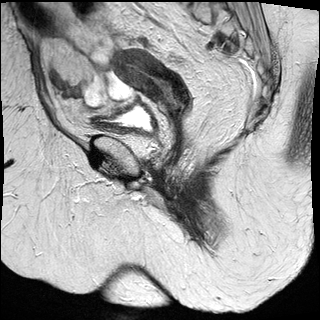
Pelvic MRI for cervical cancer, one sagittal slice. Position 12 of 27 along the scan axis. T2-weighted. 1.5 T. TE 89 ms, TR 2740 ms. 4 mm slice thickness. 320 × 320 image matrix, field of view 260 × 260 mm. Patient: female, 67 years.
Annotated regions visible in this slice (expert manual segmentation):
- uterus and cervix: box from (x=111, y=48) to (x=192, y=119) px